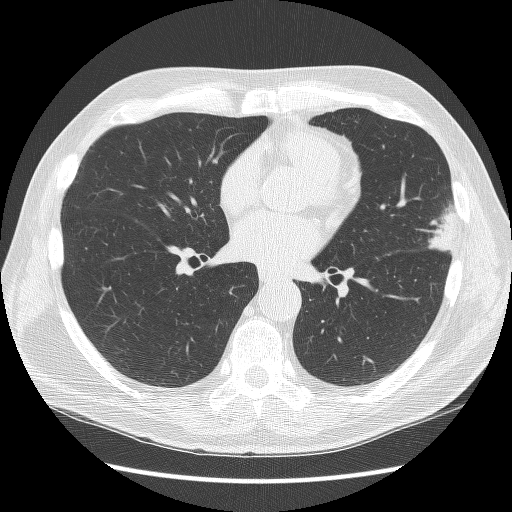
Low-dose screening chest CT, axial slice; third screening round (two years after baseline); lung window (W 1500 / L -600 HU); 2.5 mm slice thickness; slice 68 of 134 in the series; 512 × 512 image matrix, field of view 350 × 350 mm. Male, age 67 years at enrolment. Former smoker at enrolment.
Expert-annotated lung lesion, bounding box (x1, y1, x2, y2) in pixels: (408, 196, 472, 268). Reader record for this screening exam (exam-level; its link to the box is not recorded): non-calcified nodule or mass ≥4 mm, left upper lobe, 22 × 17 mm, poorly defined margins, soft tissue attenuation, pre-existing on the prior screen: yes; interval growth: yes.